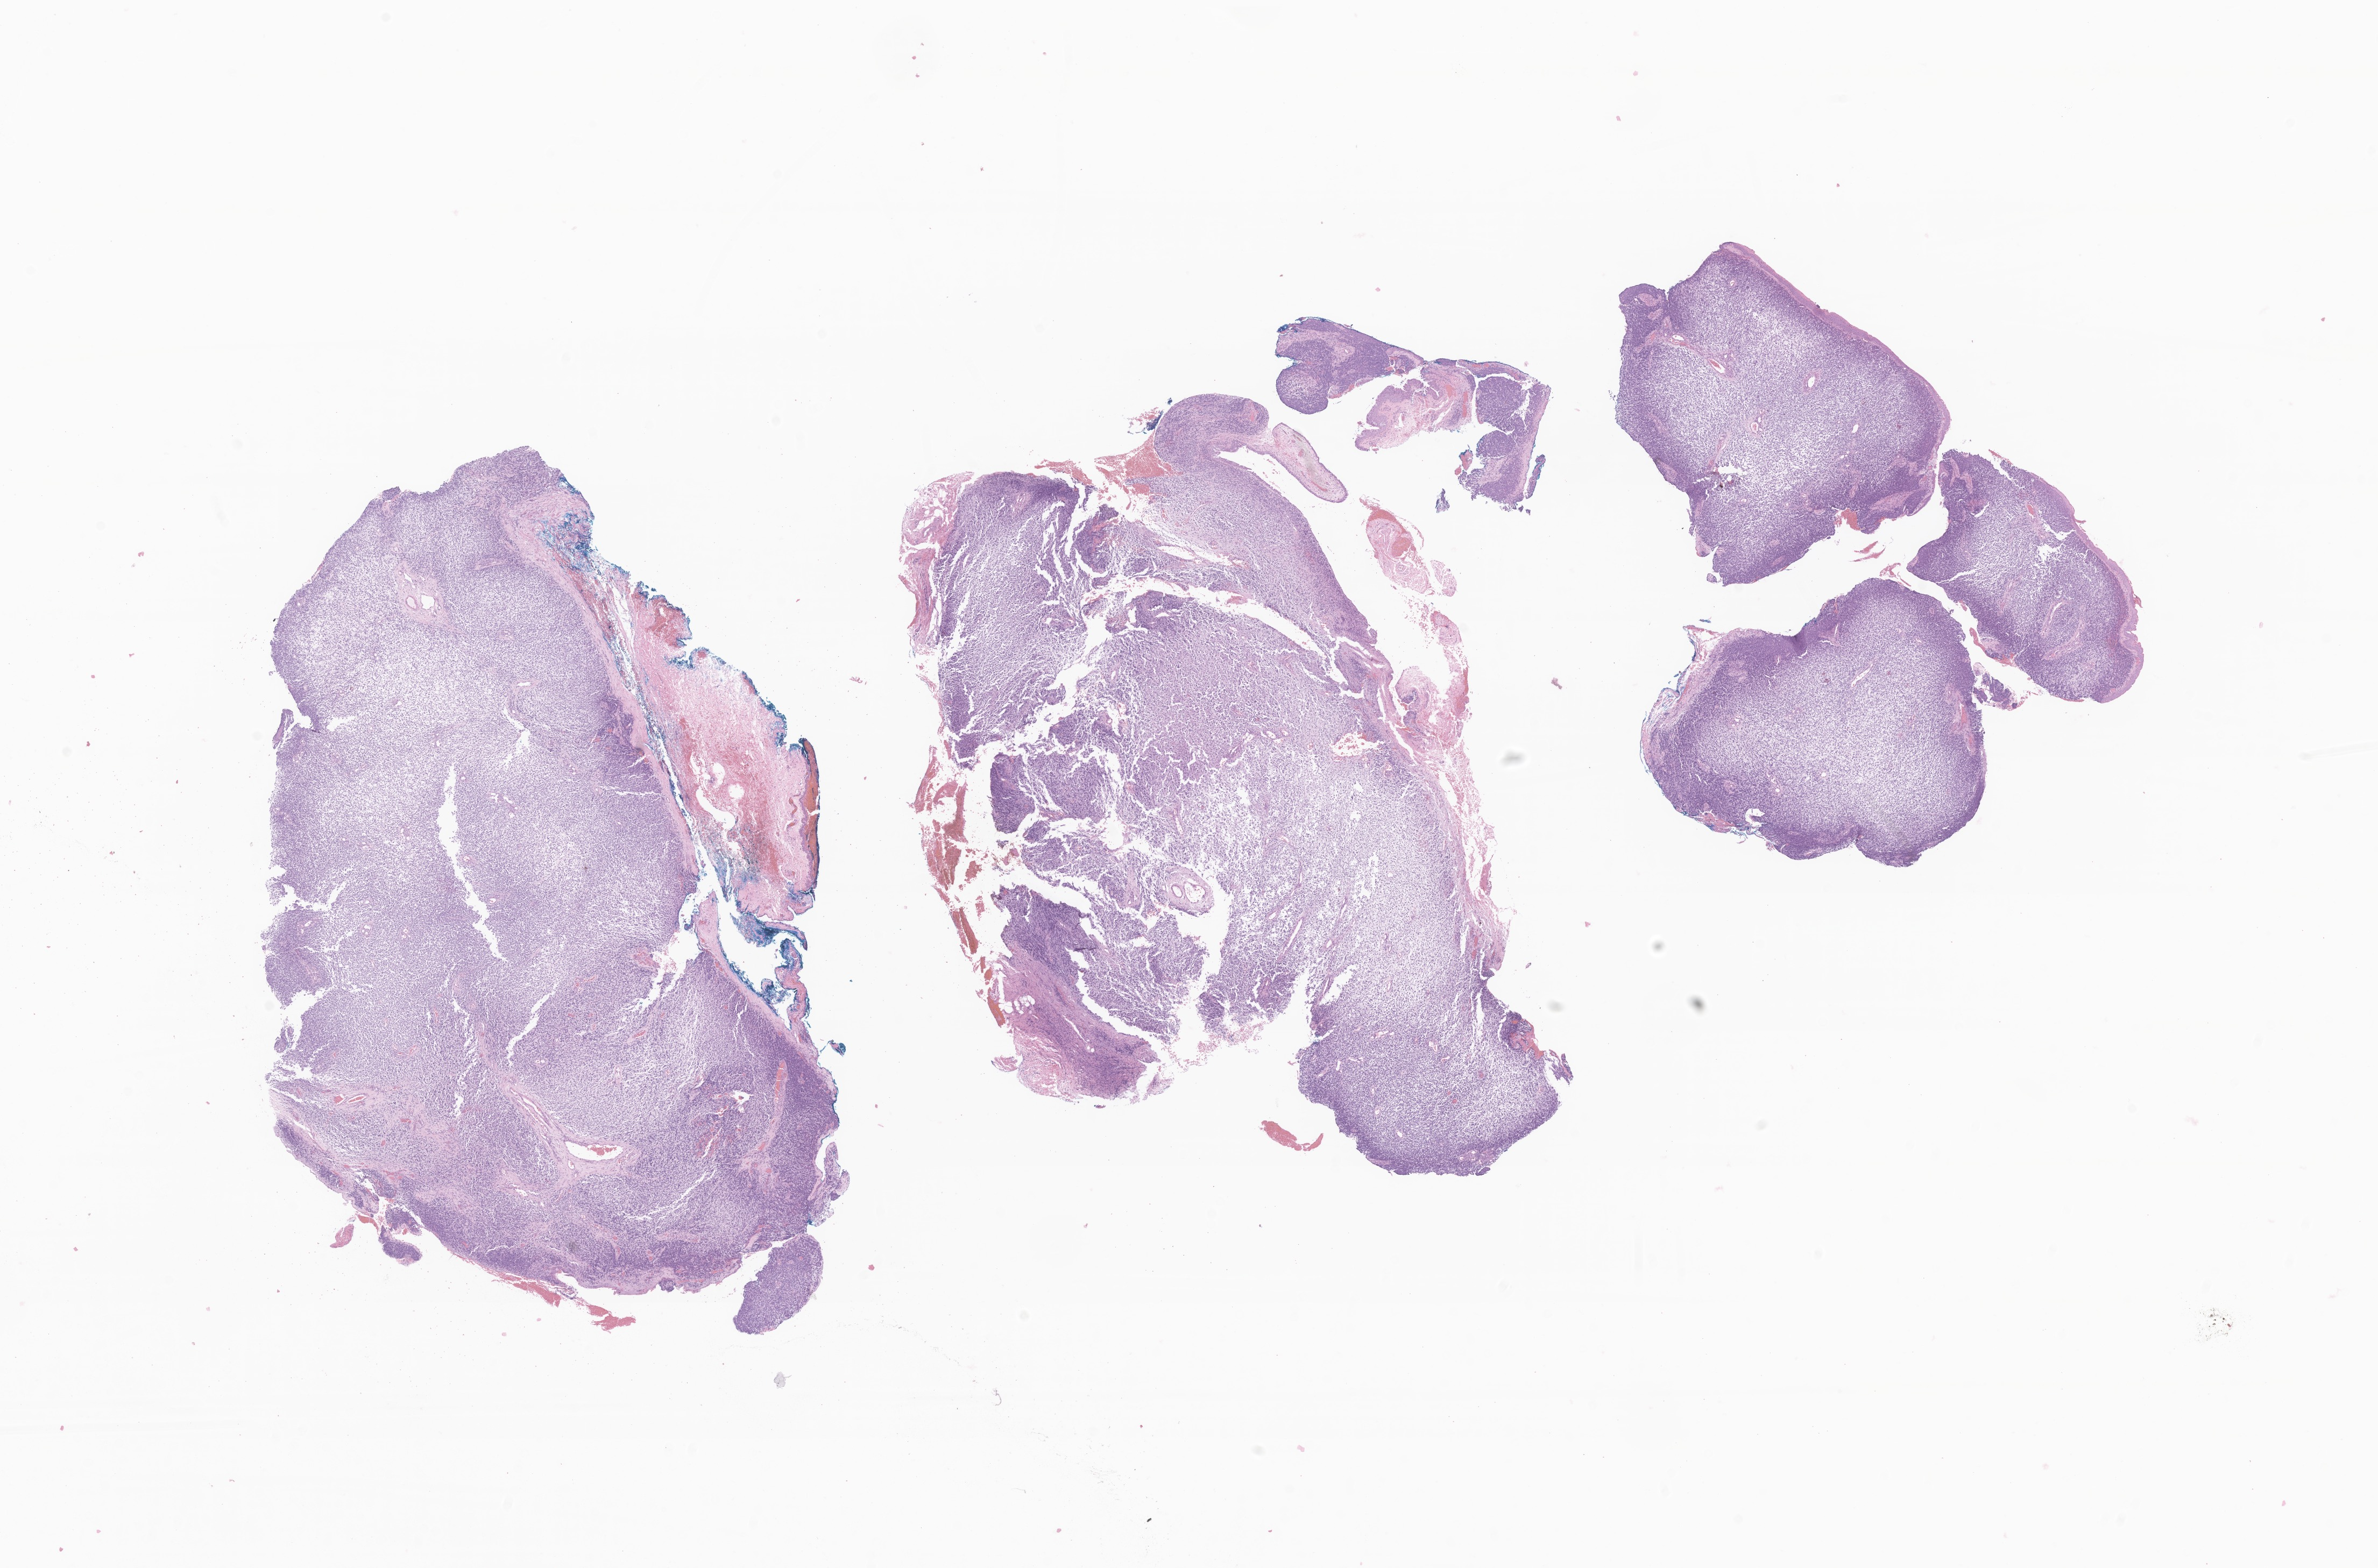
Whole-slide image, haematoxylin and eosin stain of tumor tissue from the eyelid — a low-resolution overview of the entire scanned area, about 18.6 x 12.3 mm, FFPE section. Patient female; age 42 months (3 years 6 months).
Diagnosis: Rhabdomyosarcoma, NOS.